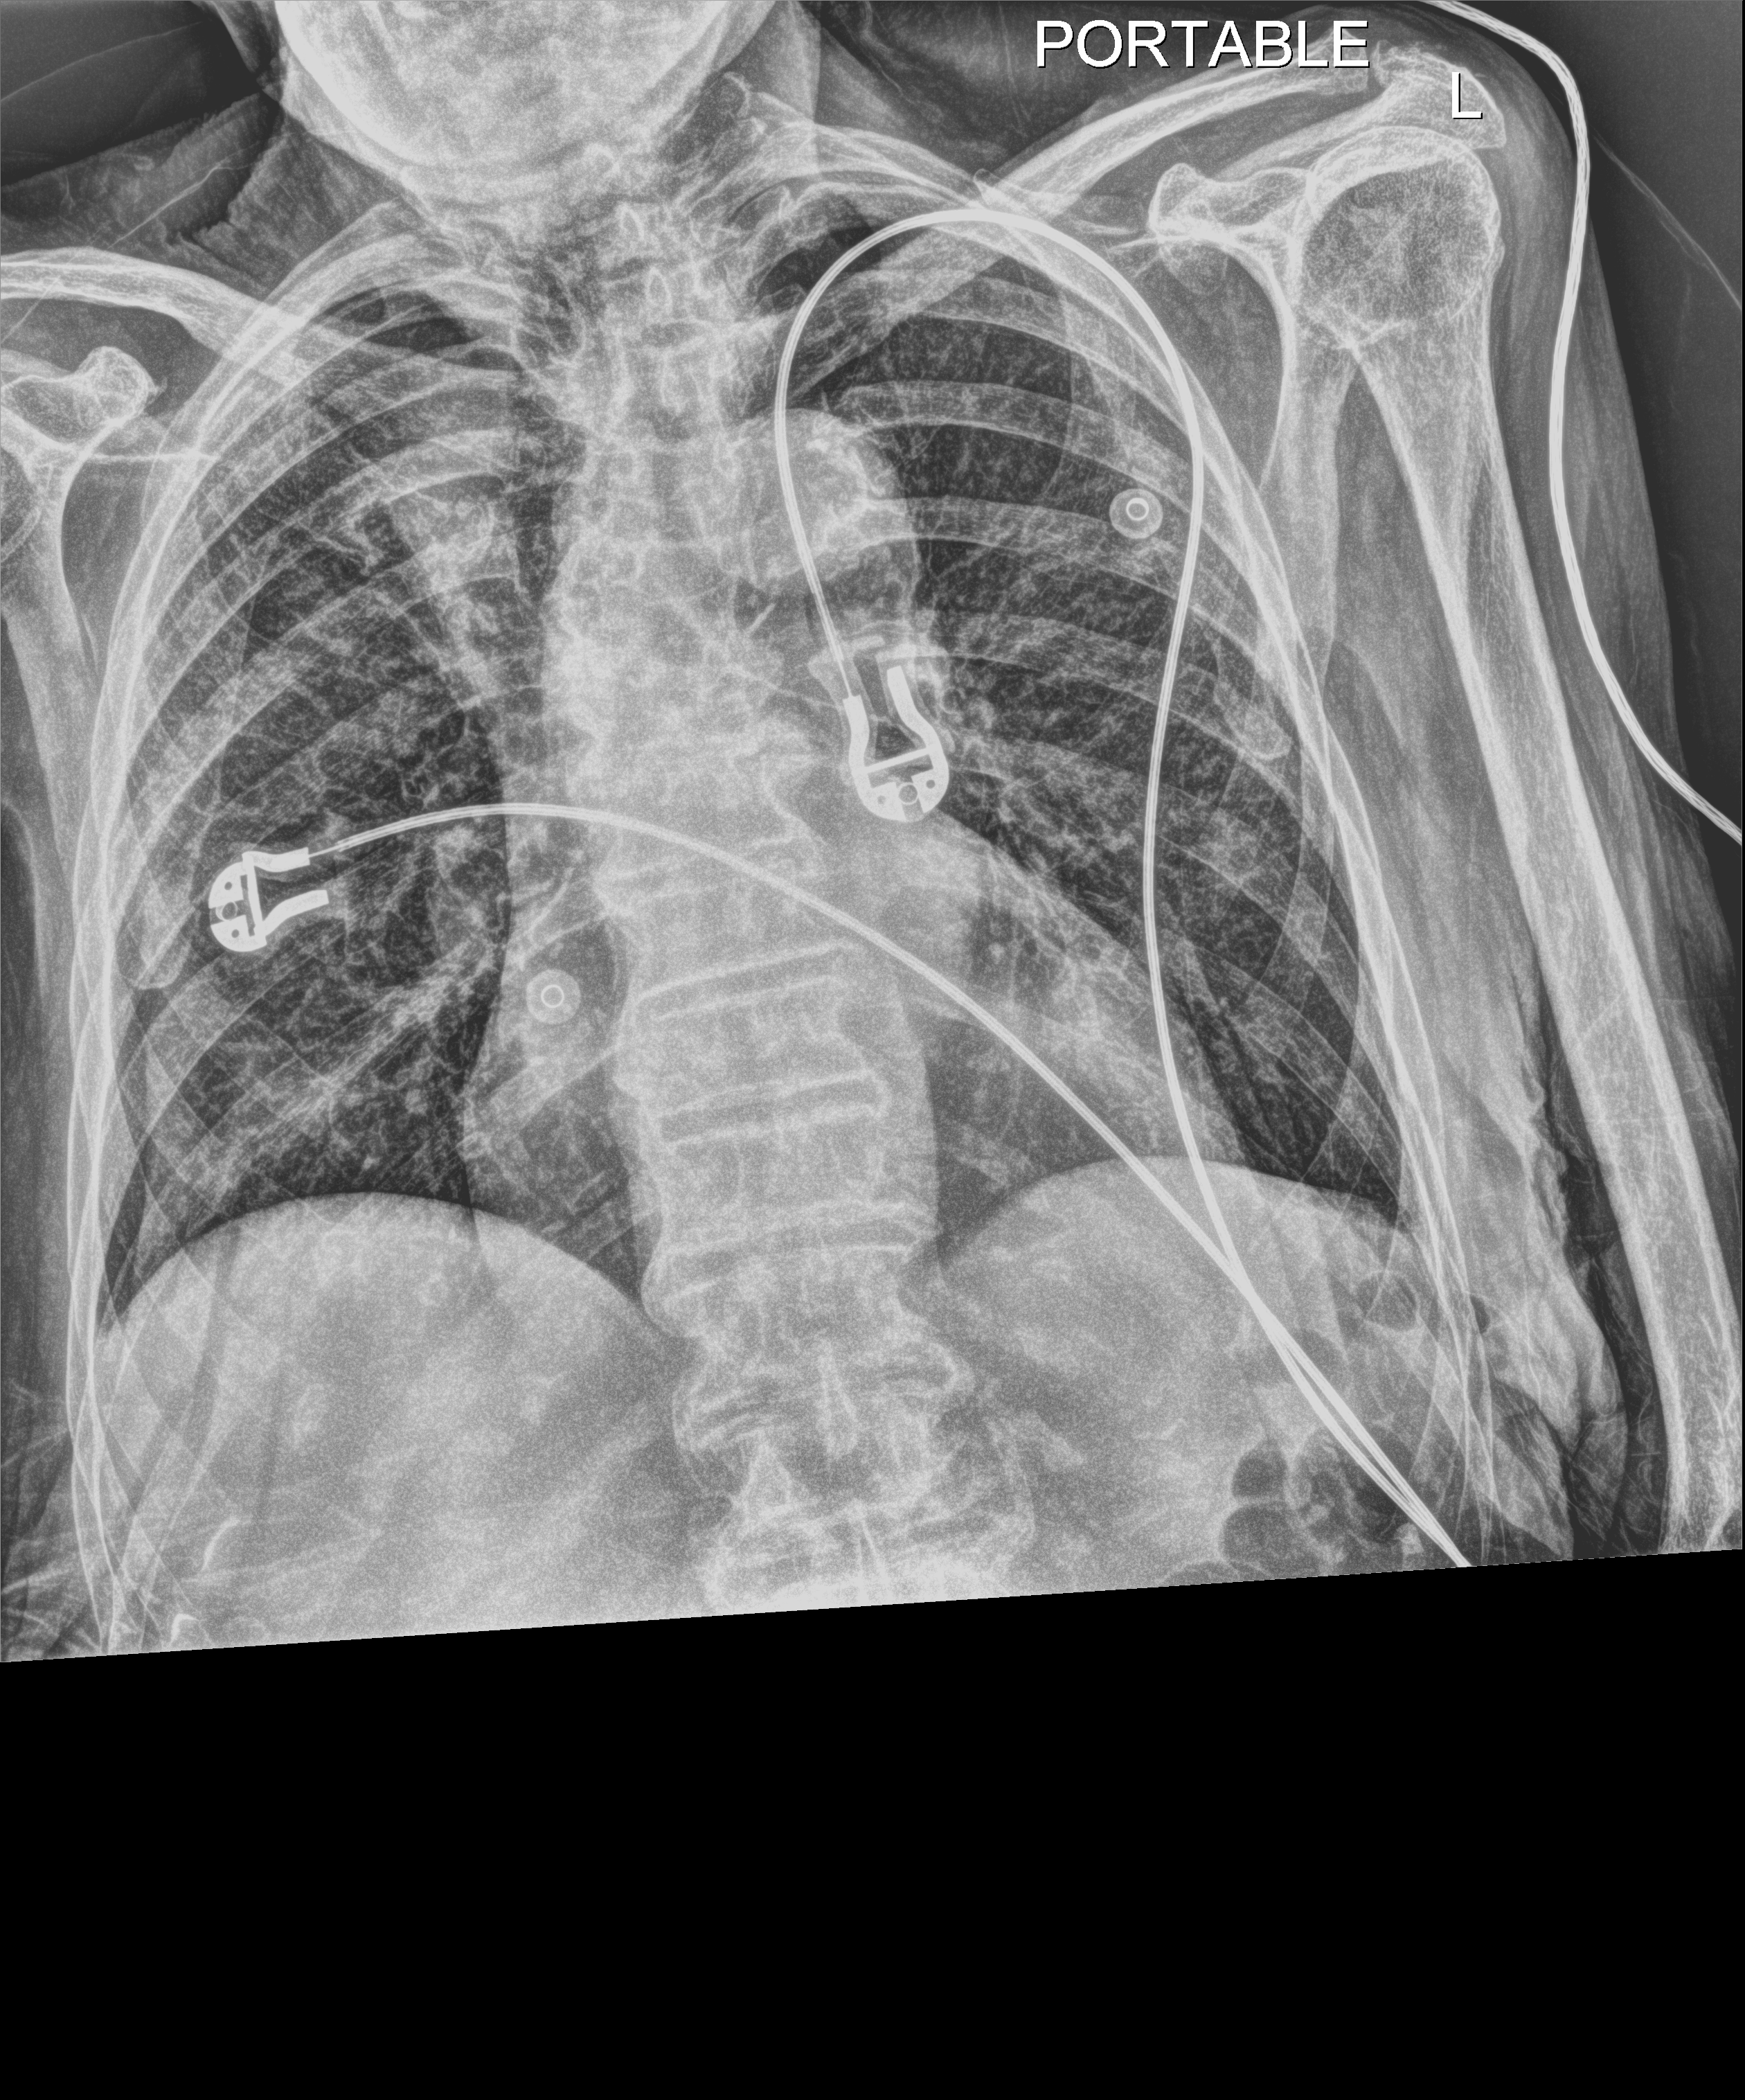
Chest X-ray; anteroposterior (AP) projection. Female patient hospitalised with COVID-19, age 75–90 years.
Admission-level facts for this patient (not findings on this image; timing relative to this image not recorded): admitted to intensive care during this hospital stay: no; mechanically ventilated during this hospital stay: no; length of hospital stay: 3 days.